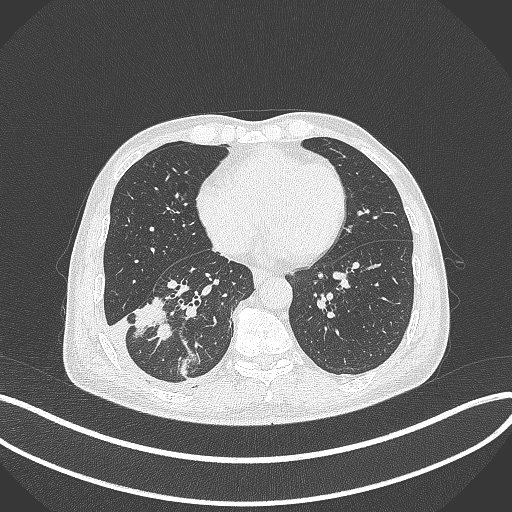
Chest CT, one axial slice; position 142 of 388 along the scan axis; lung window (W 1500 / L -600 HU); 1 mm slice thickness; 512 × 512 image matrix, field of view 400 × 400 mm. Patient: male, 64 years. Case-level facts recorded for this patient, not image findings: clinical TNM (as recorded): T3 N0 M0; histopathological grade: G2-3.
Outlined on this slice (bounding box drawn by a radiologist):
- lung tumour (recorded histology: adenocarcinoma): bounding box (x1, y1, x2, y2) in pixels: (132, 296, 176, 352)